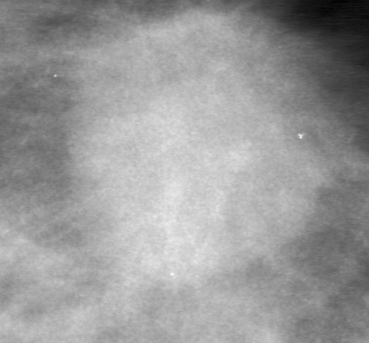
Cropped region of a digitized screen-film mammogram centred on a radiologist-marked abnormality; left breast; CC view.
Finding: mass, shape oval, margins microlobulated; BI-RADS assessment category 0 (incomplete: needs additional imaging); subtlety rating 4 on a 1 (subtle) to 5 (obvious) scale; pathology result (as recorded, not read from the image): malignant.